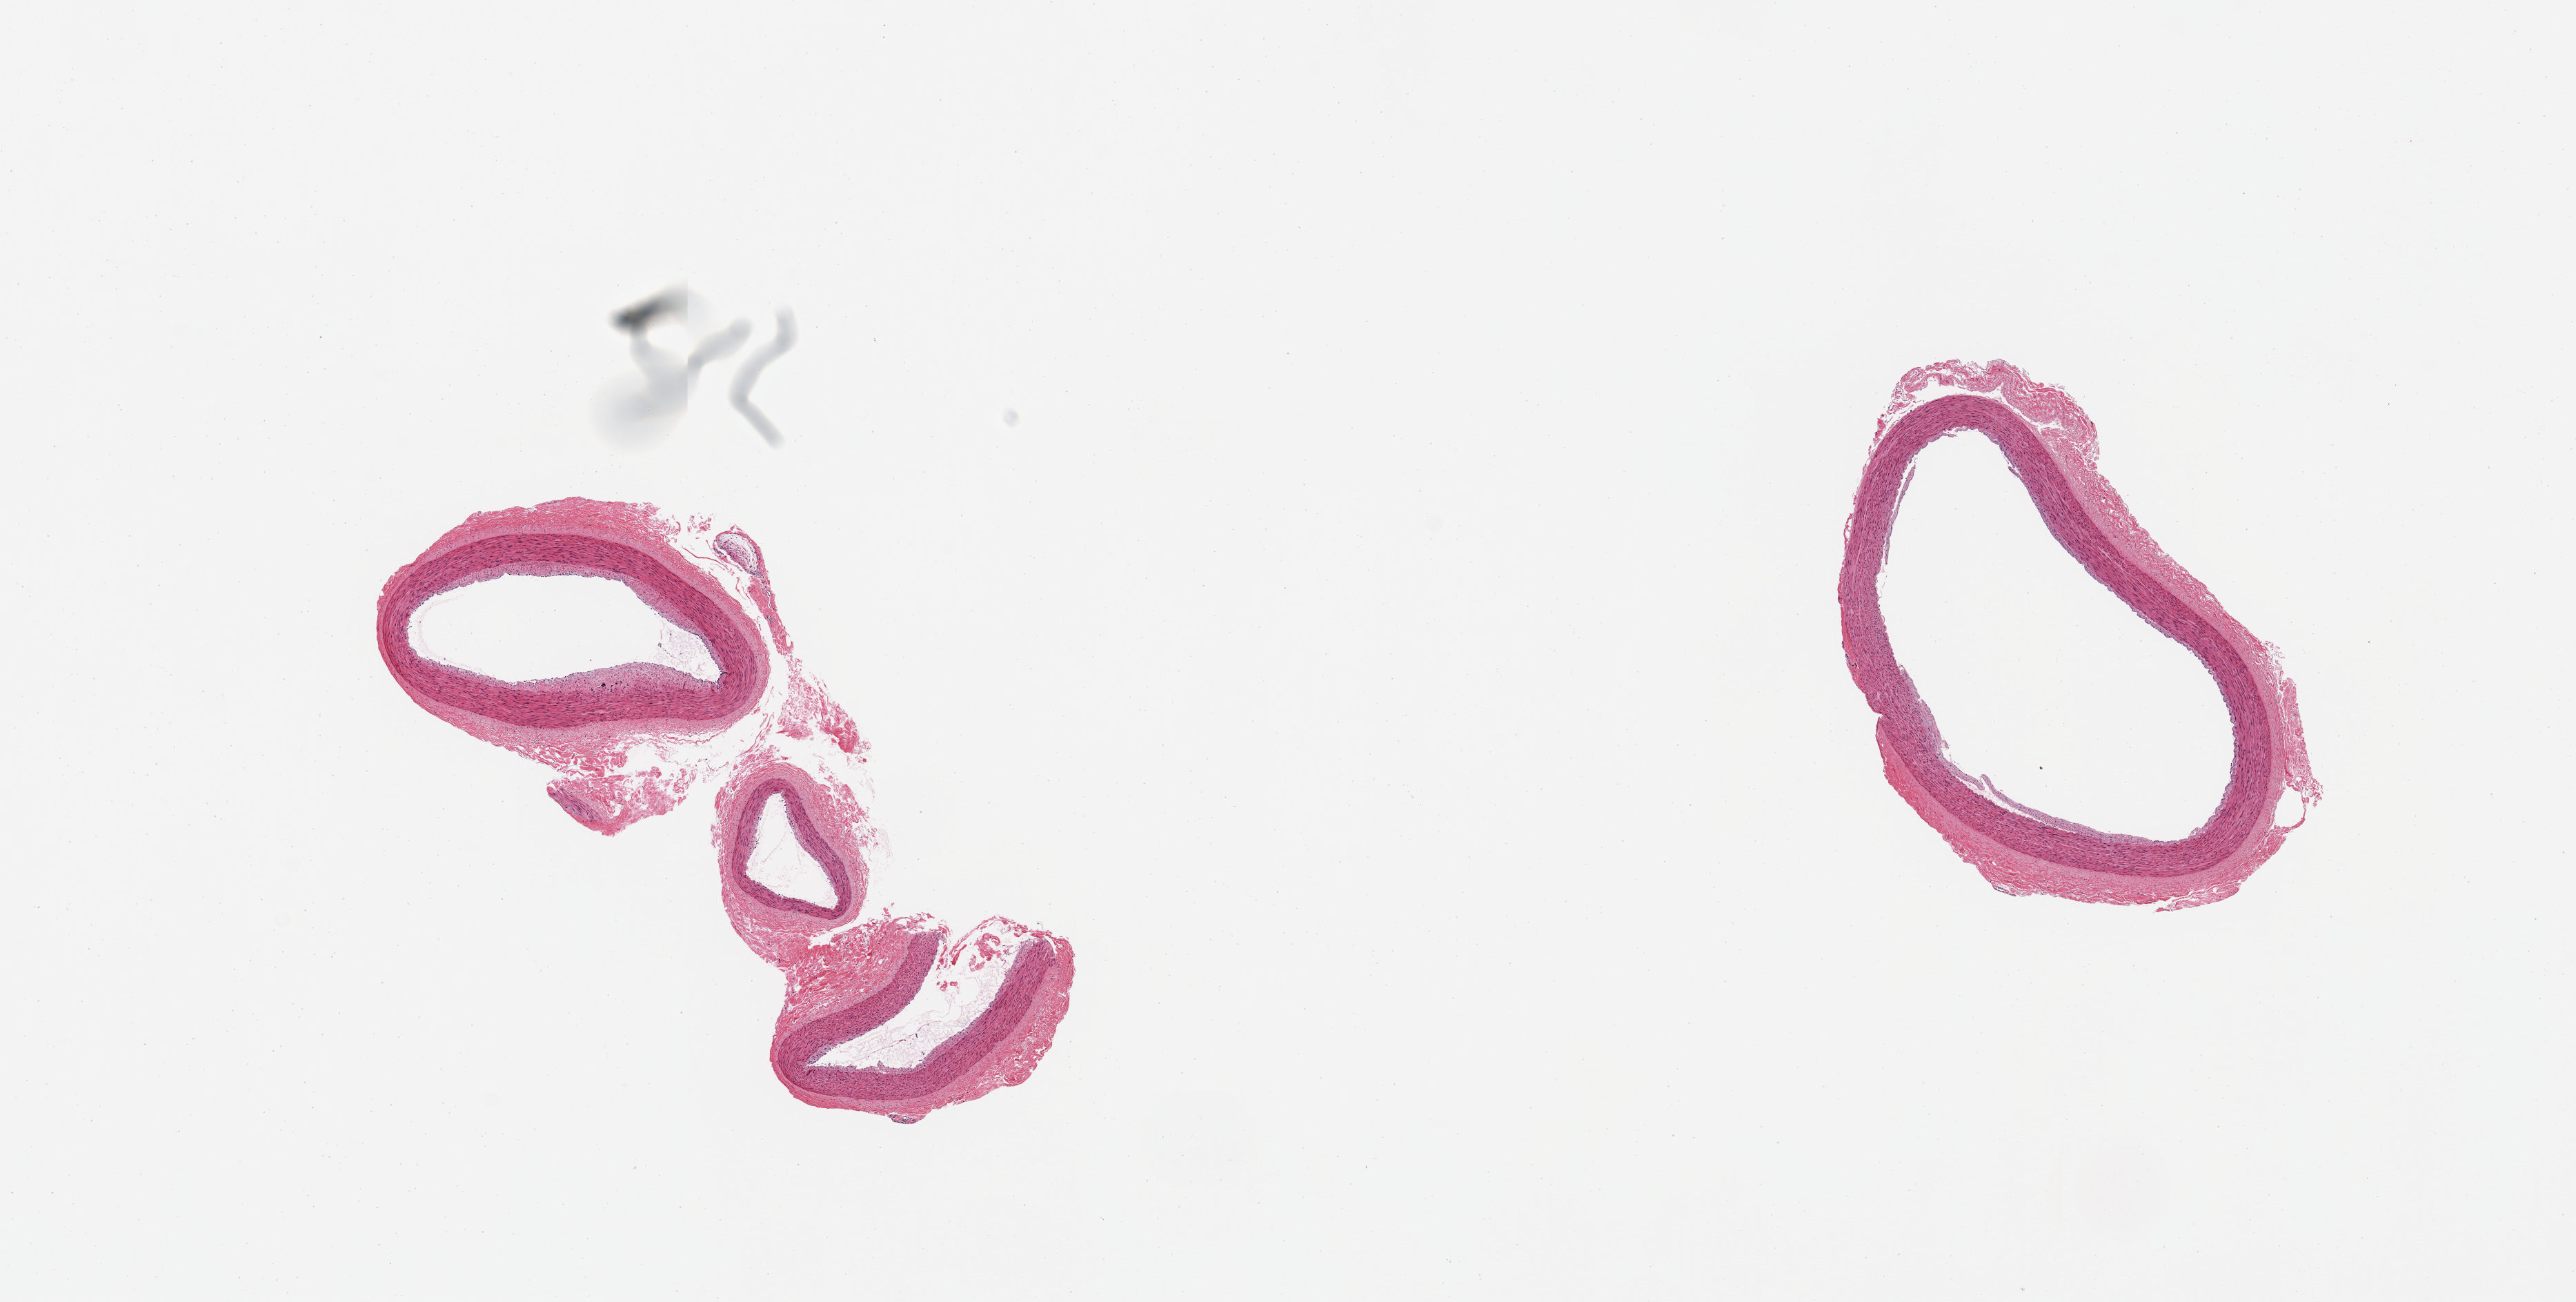
Digitized H&E-stained section, low-resolution overview of the scanned area, about 14.8 x 7.5 mm (from a 20x scan). PAXgene-fixed, paraffin-embedded tissue. Sampled site (target tissue): tibial artery. Donor tissue sample. Donor sex: female.
Pathologist's review note for this sample: 2 pieces; trivial medial calcification and intimal thickening.